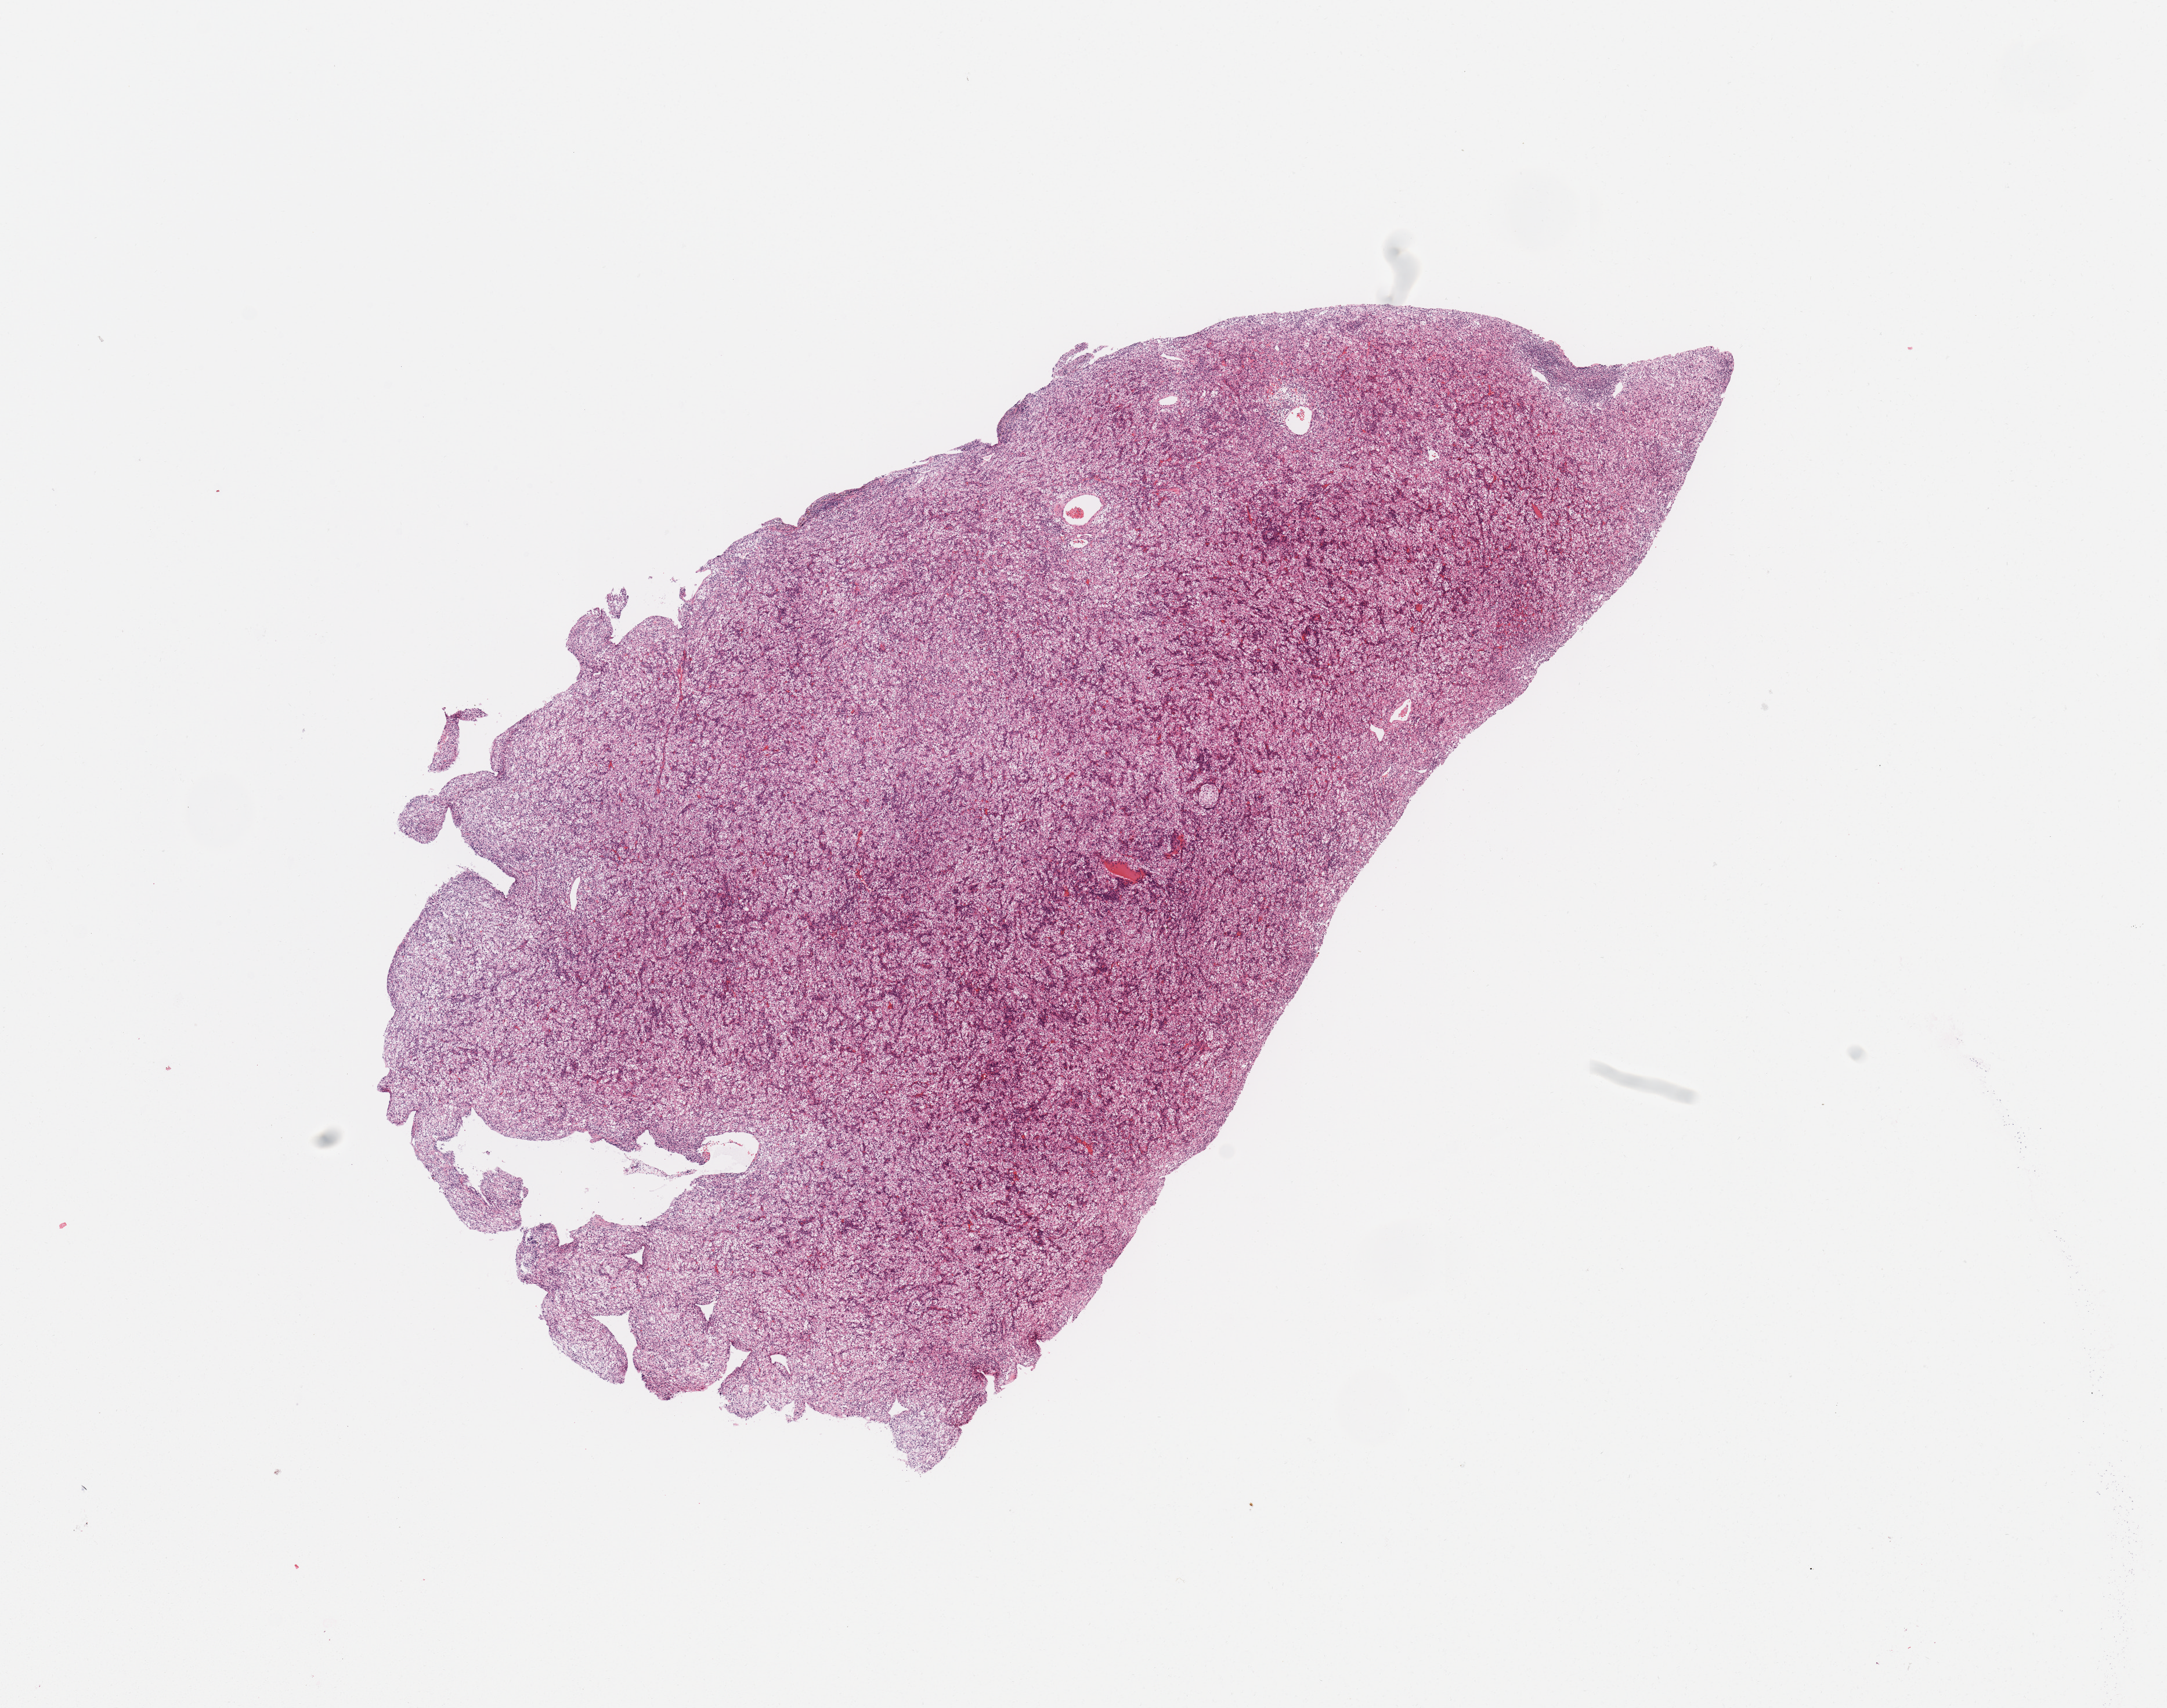
Whole-slide histology image, Hematoxylin and eosin (H&E) stained — whole scanned area (about 14.8 x 11.6 mm) shown as a low-resolution overview; tumour tissue sample, sampled site: kidney. 47-year-old male patient. Histologic grade: G2 (moderately differentiated). Pathologist review of this section (percent, as recorded): tumour nuclei 80%, necrosis 2%.
* histologic diagnosis: Renal cell carcinoma, NOS
* primary tumour site (as recorded): upper pole
* AJCC pathologic stage: I